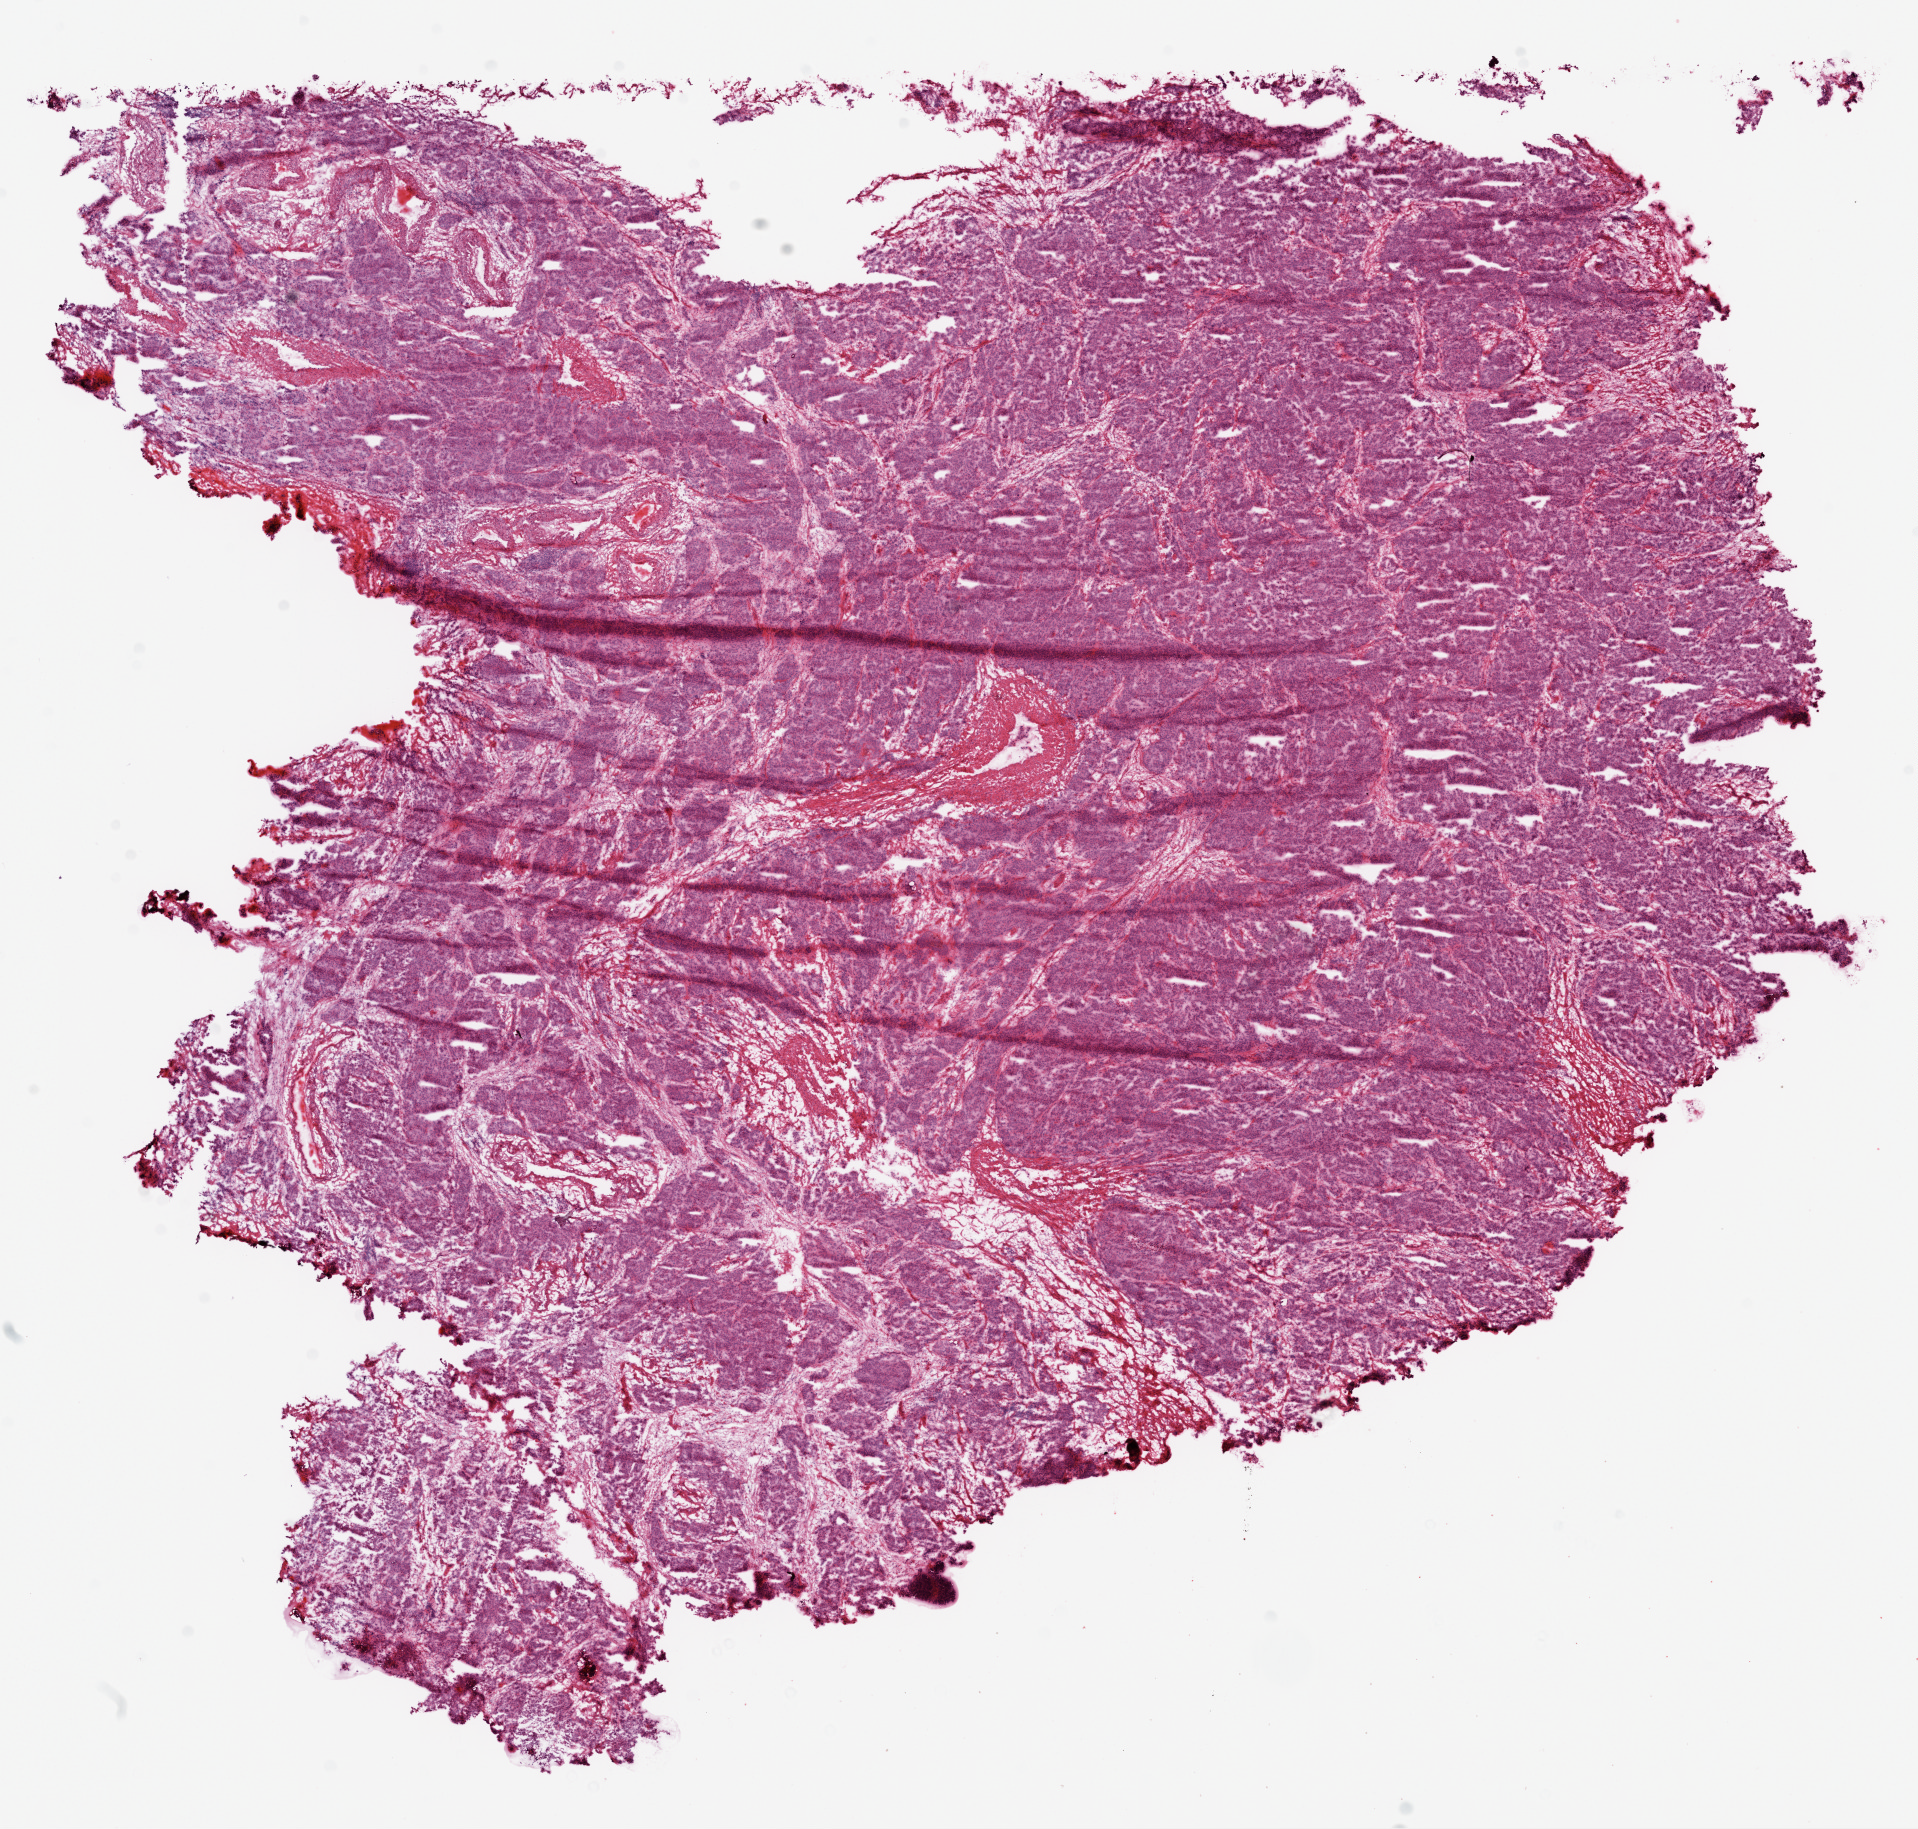
Digitized H&E-stained tissue section (whole slide), low-resolution overview of the scanned area, about 15.5 x 14.8 mm (from a 20x scan); frozen section; sample: primary tumour, ovary. Female, age 77 years at initial diagnosis. Histologic grade: G3 (poorly differentiated). Slide review estimates, as recorded: tumour cells 95%, tumour nuclei 95%, normal cells 0%, stromal cells 5%, necrosis 0%.
- pathologic diagnosis: Serous cystadenocarcinoma, NOS
- FIGO stage: IV